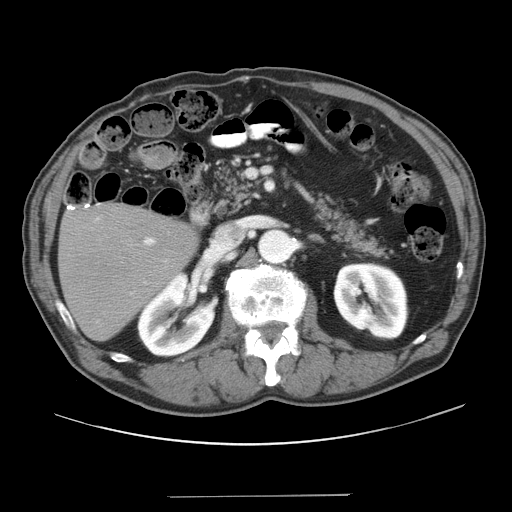
Contrast-enhanced abdominal CT, one axial slice; position 17 of 41 along the scan axis; reconstruction kernel STANDARD; 120 kVp; intravenous contrast given; soft-tissue window (W 400 / L 40 HU); 512 × 512 image matrix. Male patient, age 75 years. From the clinical record (not read from this slice): diagnosis: colorectal cancer liver metastases, imaged before liver resection; multiple liver metastases: no; largest metastasis: 5.2 cm.
Outlined on this slice (expert manual segmentation):
- liver: box from (x=60, y=205) to (x=197, y=340) px
- planned liver remnant (the part of the liver to remain after resection): (x=60, y=205)–(x=196, y=341)
- portal vein (with intrahepatic branches): (x=131, y=237)–(x=167, y=294)